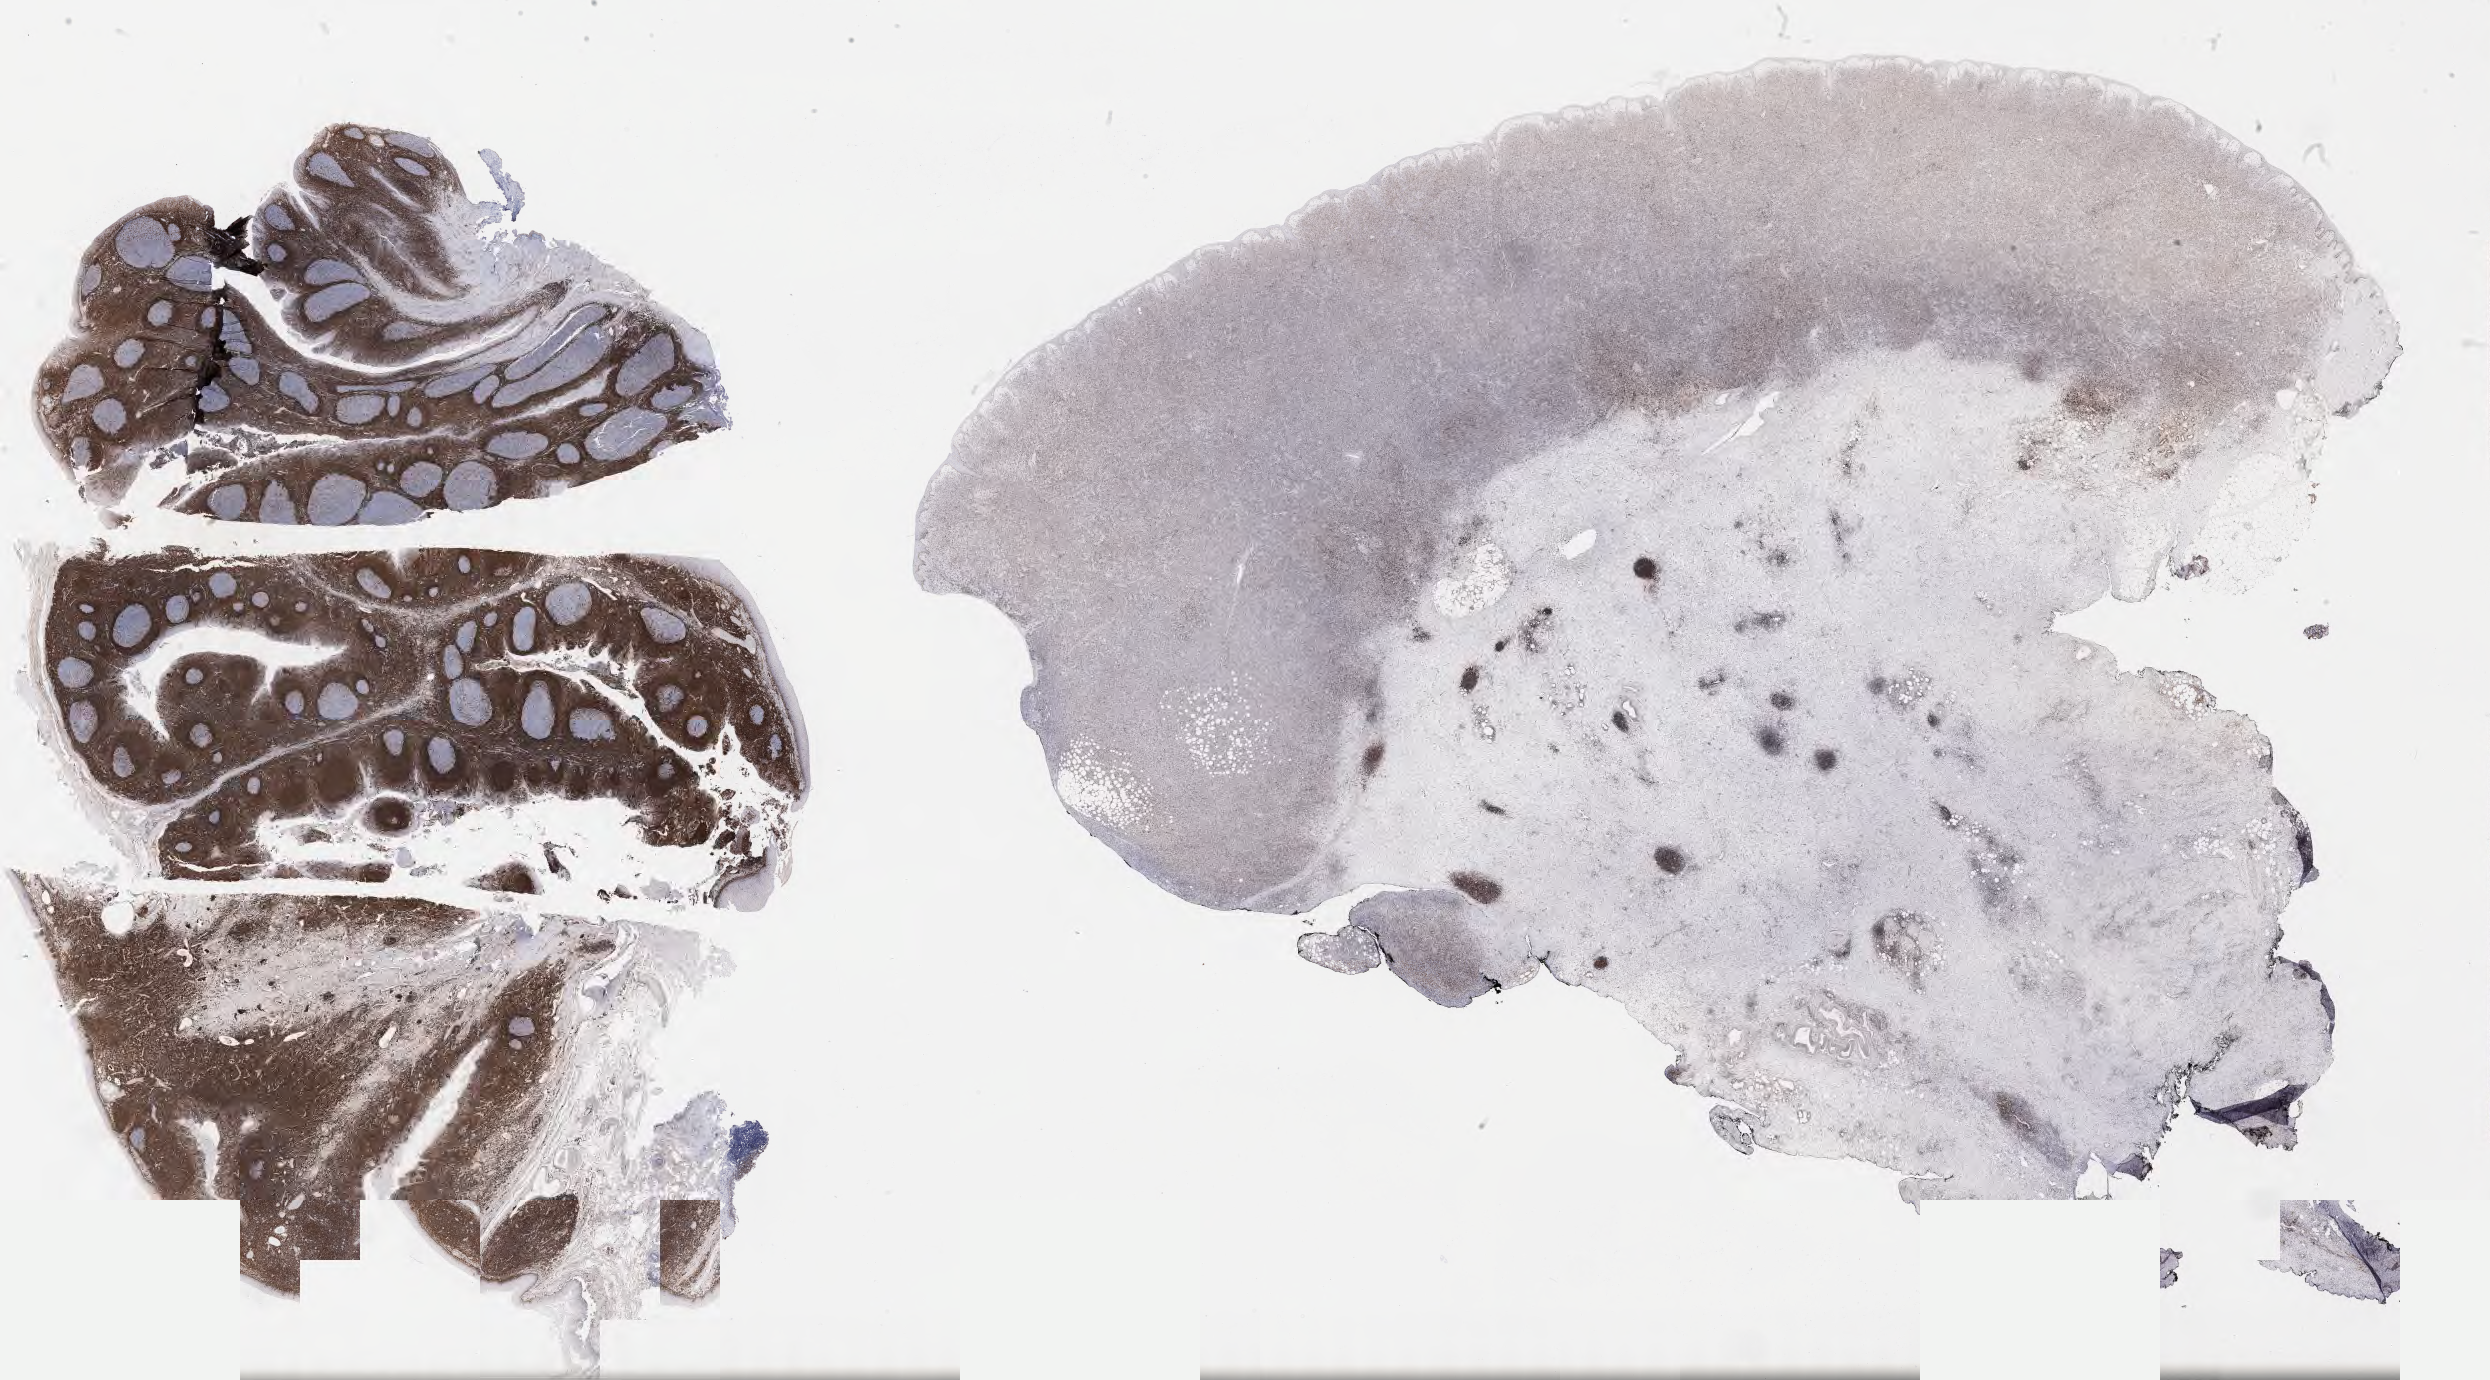
IHC for BCL2, whole-slide image, shown as a low-resolution overview of the whole scanned area (about 40.2 x 22.3 mm), tumor tissue, site: lymph node. Patient male; aged 52.
Histologic diagnosis: Diffuse large B-cell lymphoma, NOS.